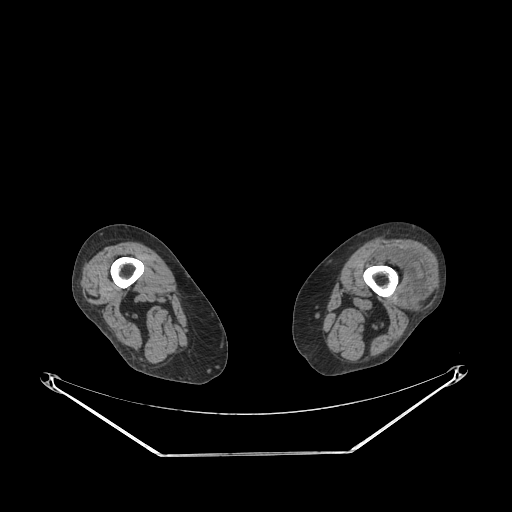
CT of an extremity soft-tissue mass (from a PET/CT study), one axial slice; slice 195 of 267 in the series (ordered by position); reconstruction kernel STANDARD; soft-tissue window (W 400 / L 40 HU); 3.75 mm slice thickness; 512 × 512 image matrix, field of view 500 × 500 mm. Female patient. Case-level facts recorded for this patient, not image findings: histological type: undifferentiated – high grade; grade: high; site of the primary tumour: left thigh.
Outlined on this slice (expert contour drawn on MRI and transferred to this co-registered scan by the dataset authors):
- gross tumour volume including surrounding oedema: box from (x=374, y=251) to (x=428, y=296) px